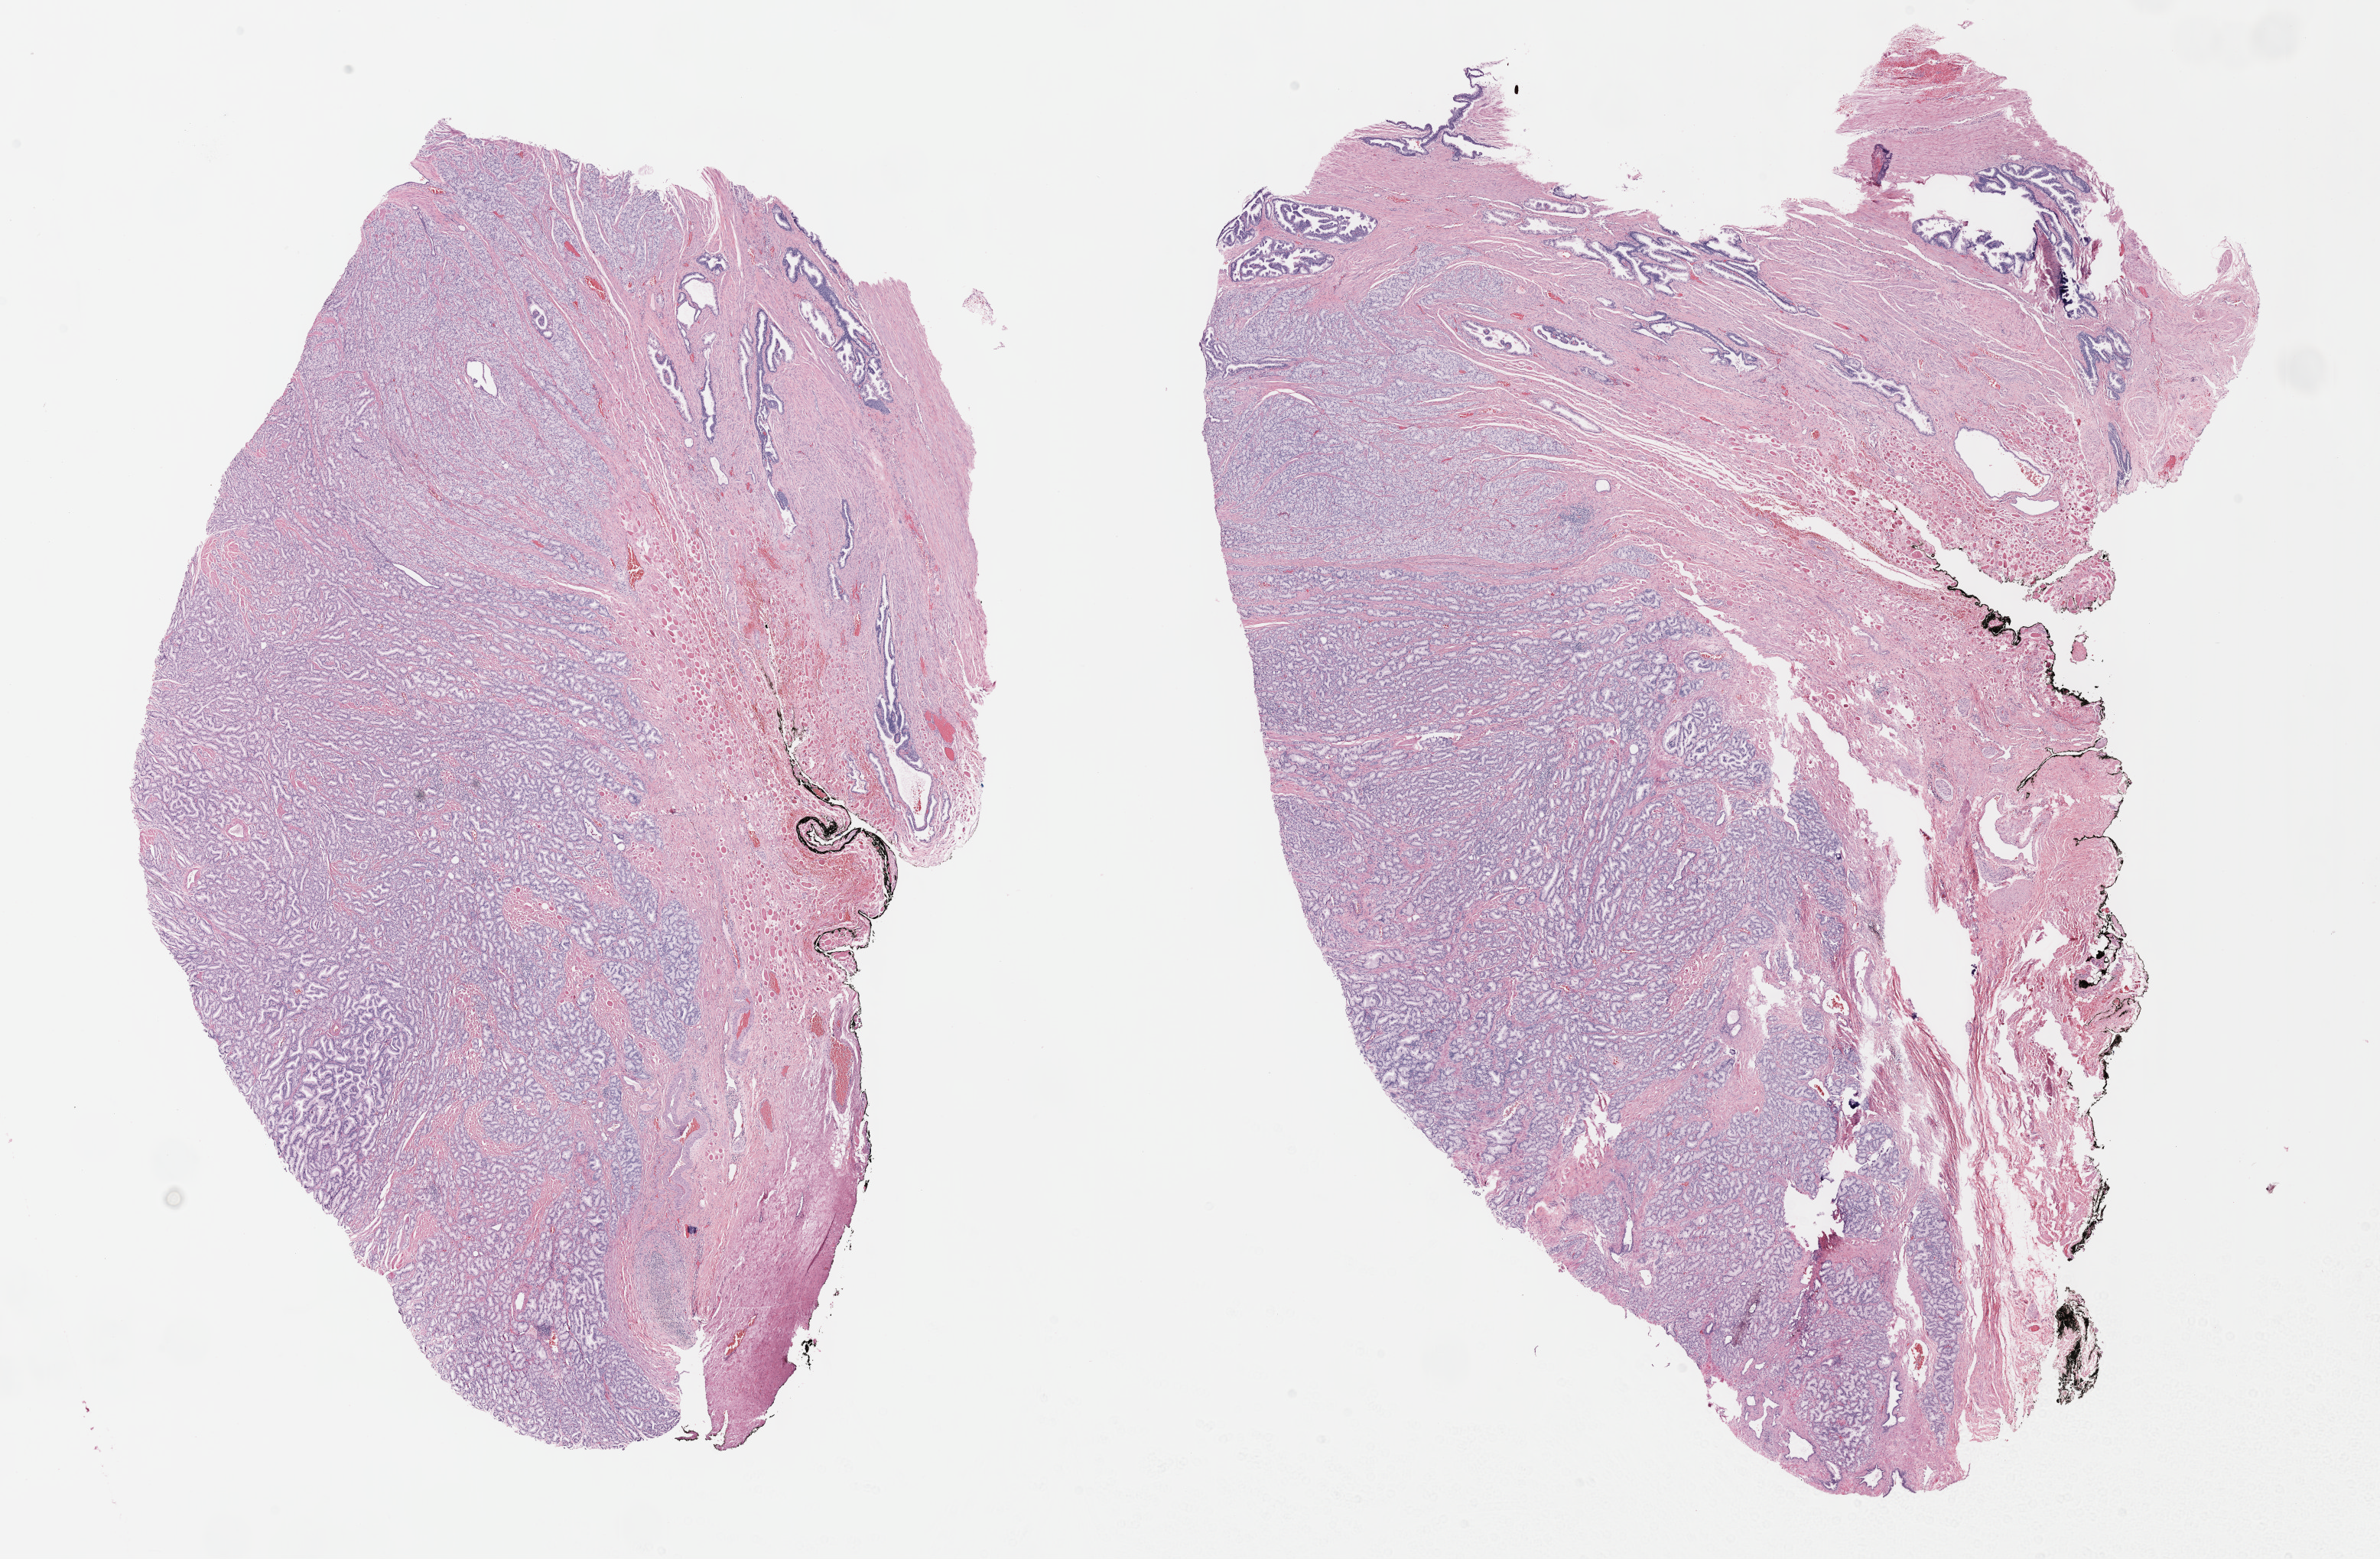
Whole-slide histology image, H&E-stained, shown as a low-resolution overview of the whole scanned area (about 25.2 x 16.5 mm, slide scanned at 40x), formalin-fixed paraffin-embedded (FFPE) diagnostic section, primary tumour sample from the prostate. Male patient; age at initial diagnosis 70 years. Gleason score: 8 (4+4).
Diagnosis: Adenocarcinoma, NOS (prostate gland).